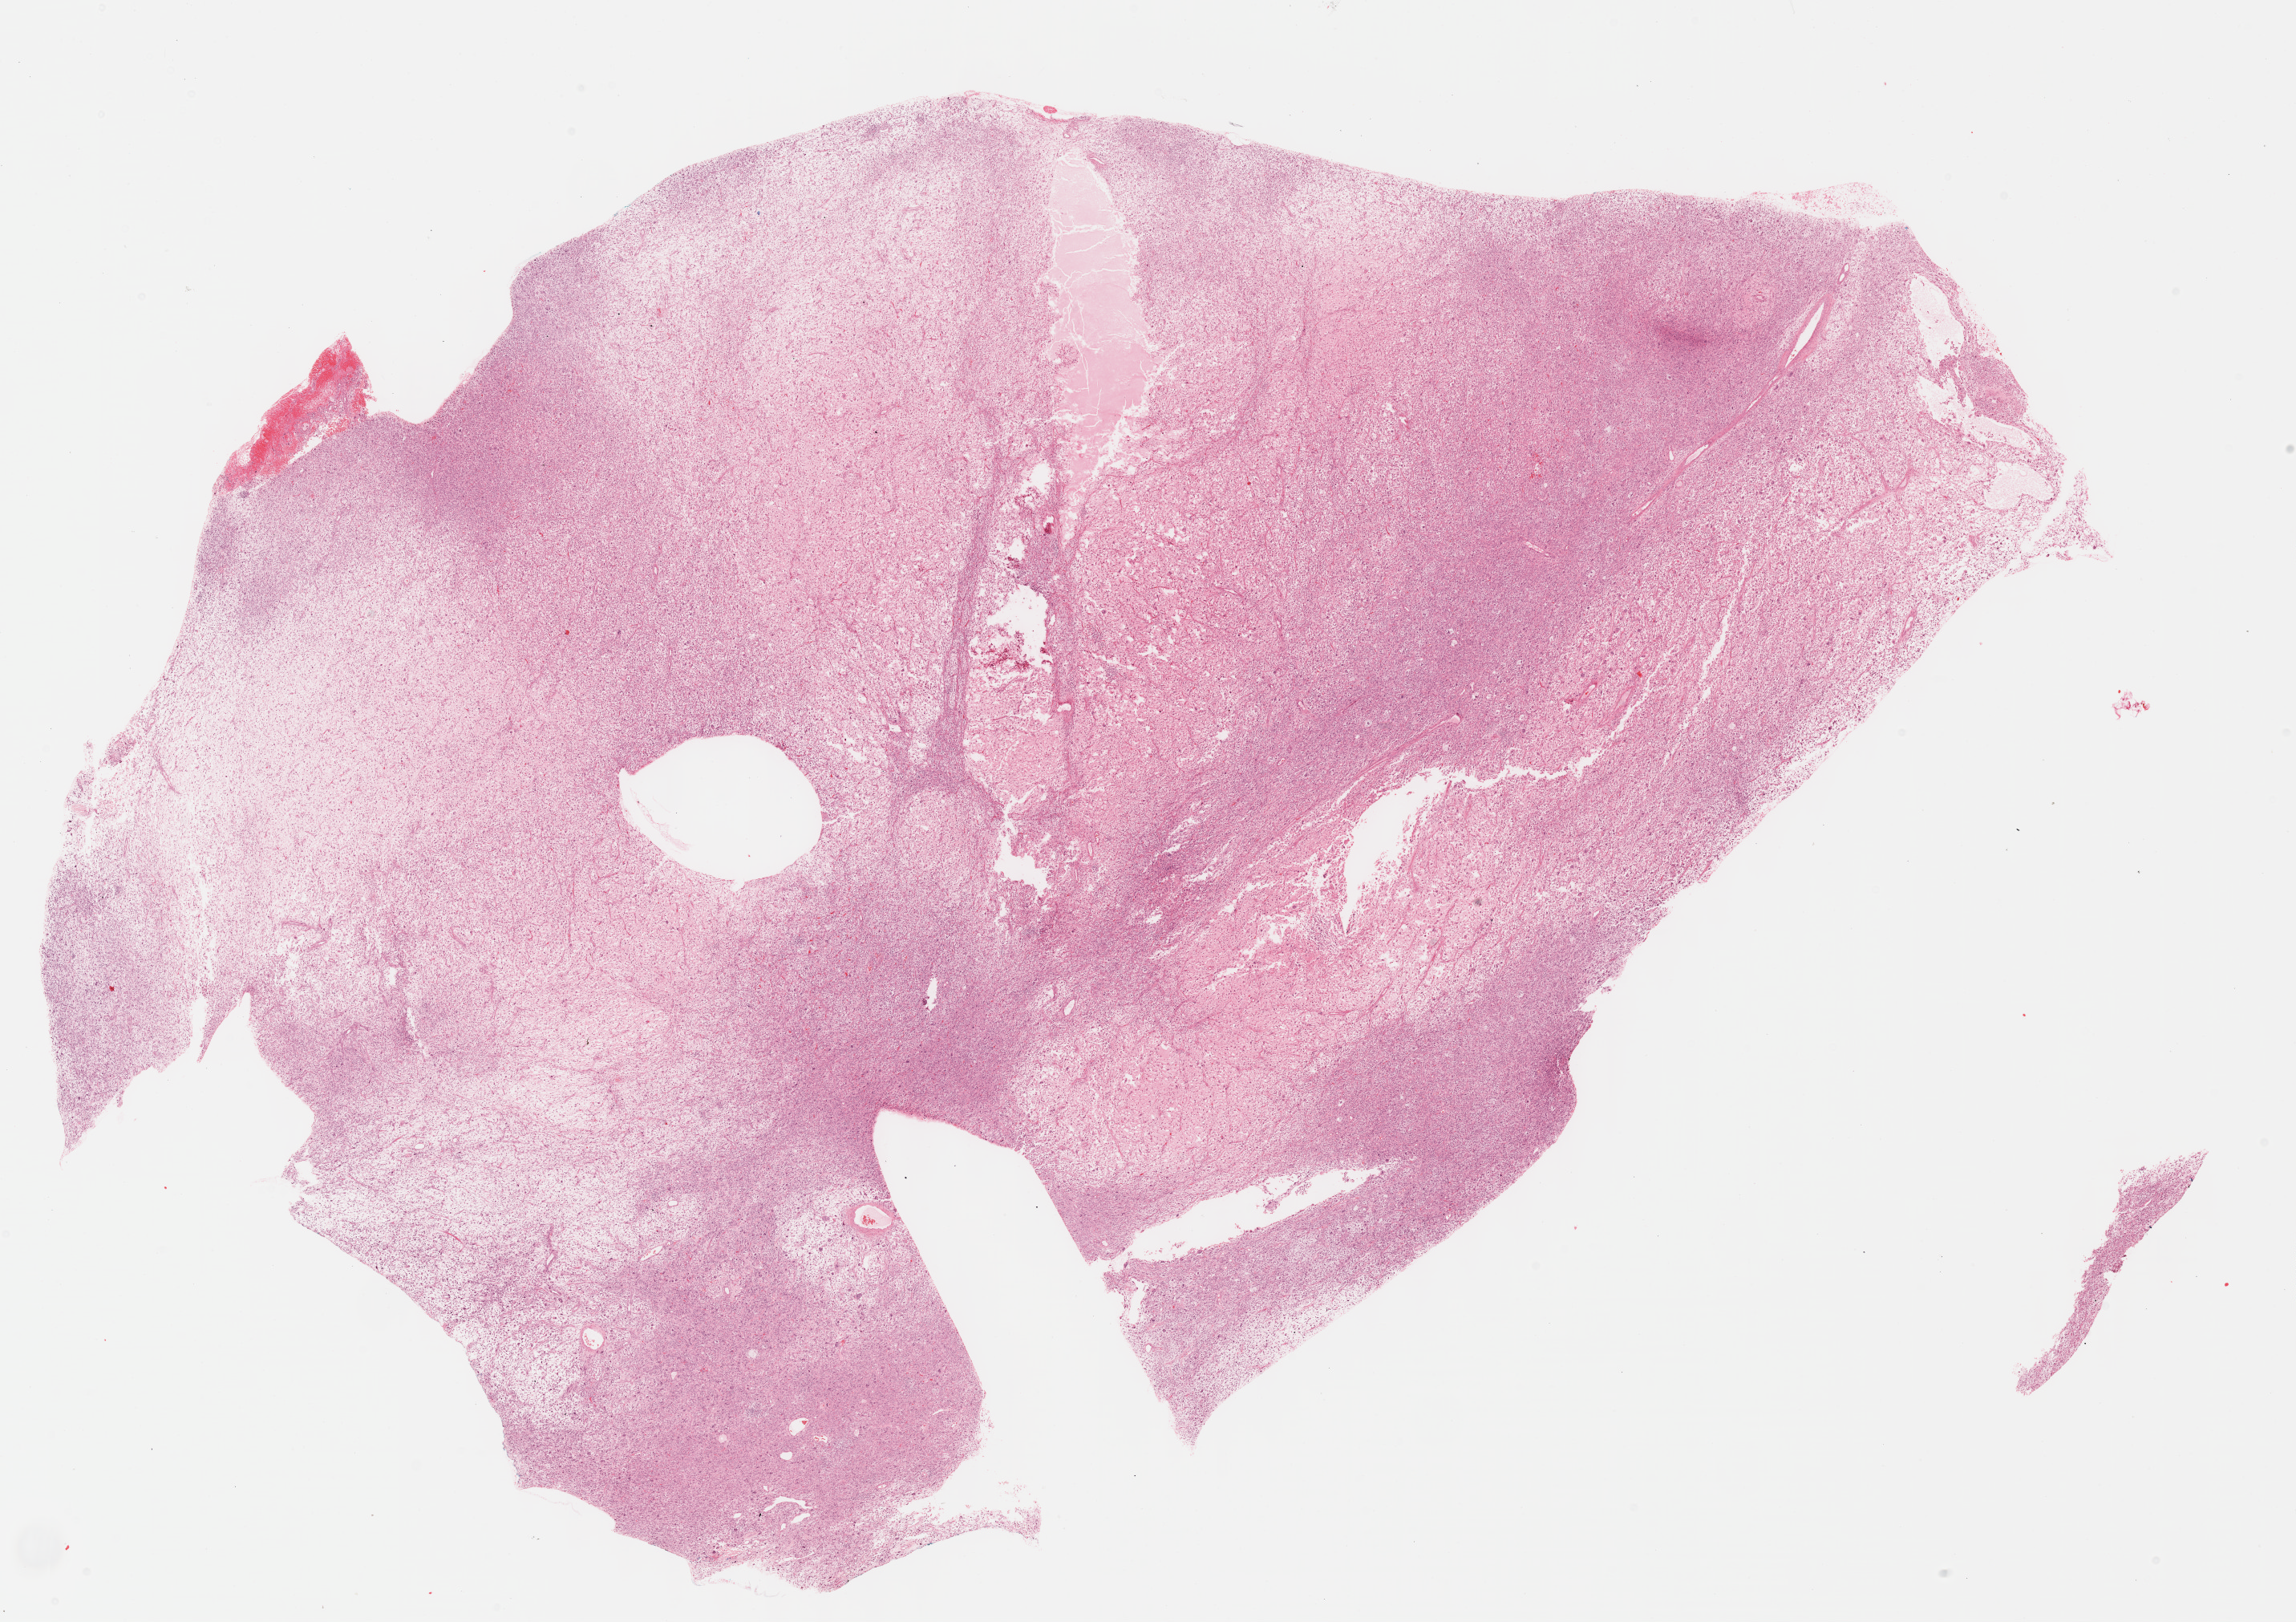
Digitized Hematoxylin and eosin (H&E) stained tissue section (whole slide) — low-resolution overview of the scanned area, about 23.1 x 16.3 mm (slide scanned at 40x), FFPE section, connective, subcutaneous and other soft tissues, primary tumour sample. Female patient; age at initial diagnosis 63 years.
Diagnosis: Malignant fibrous histiocytoma (connective, subcutaneous and other soft tissues of lower limb and hip).